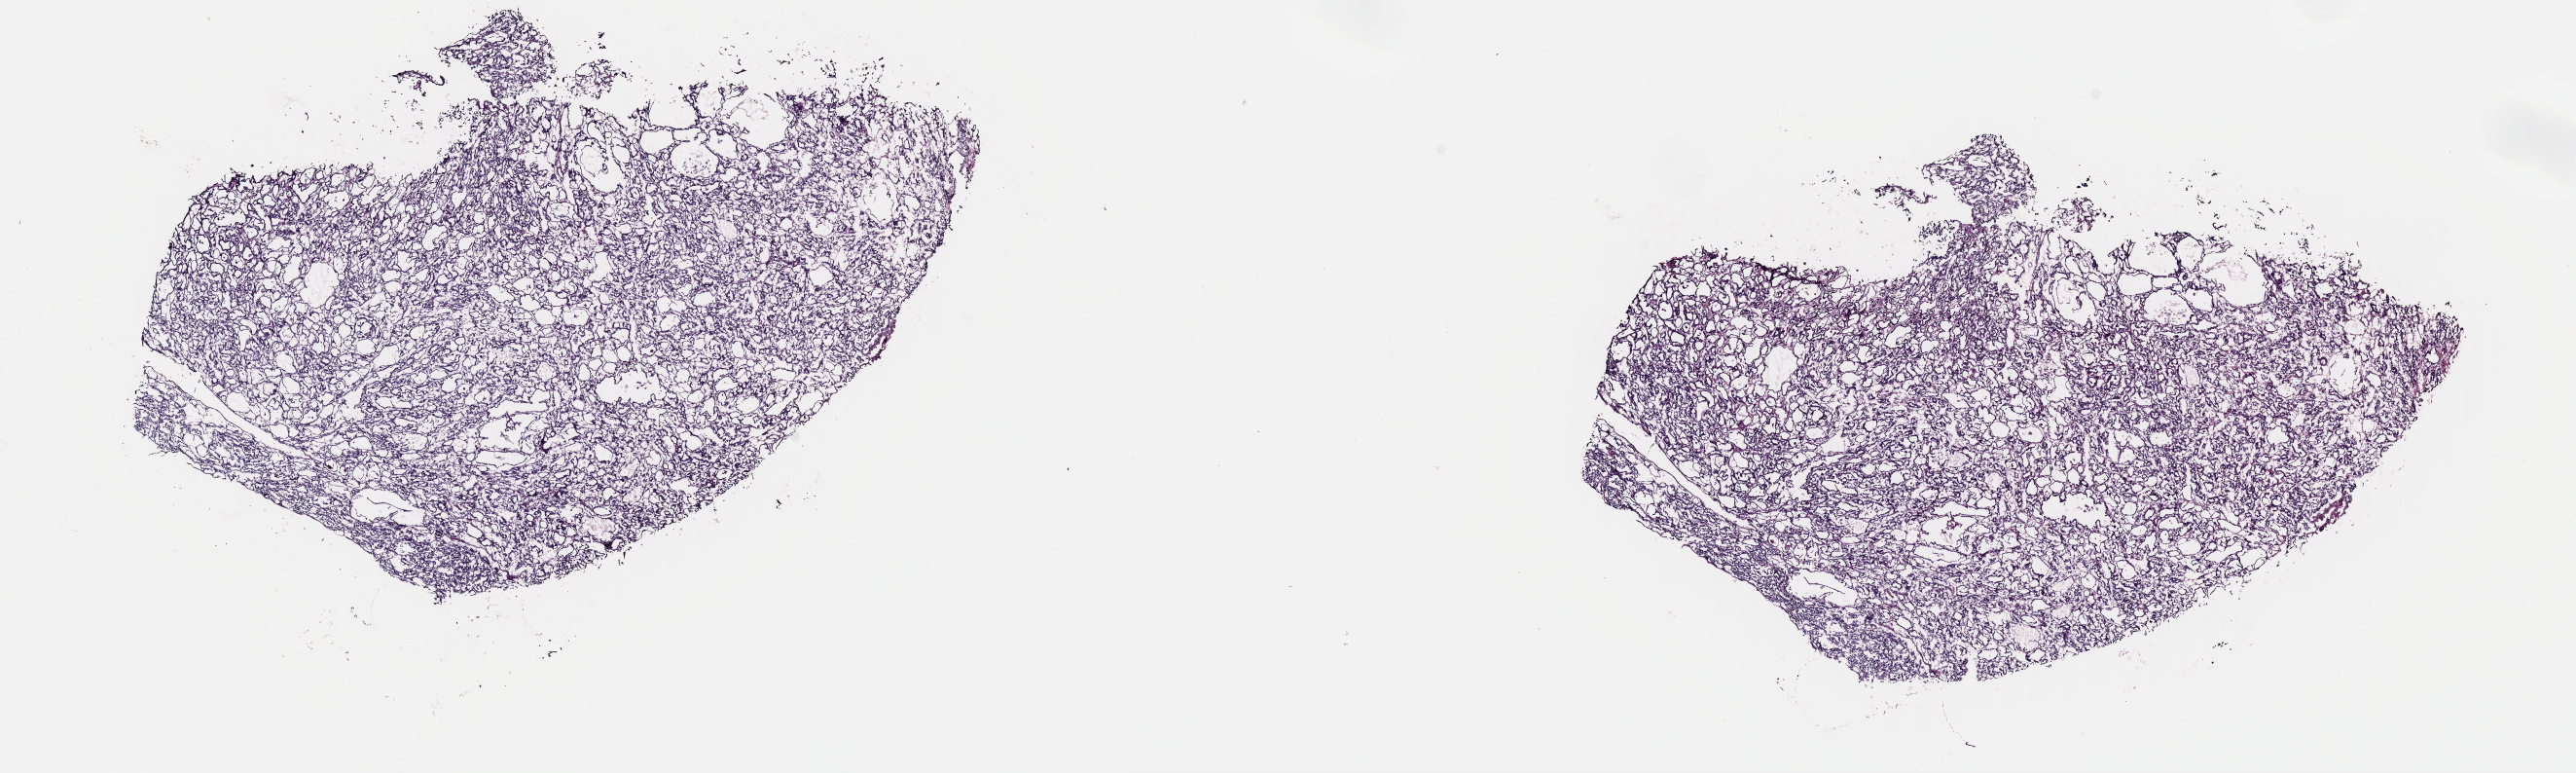
H&E-stained whole-slide image, a low-resolution overview of the entire scanned area, about 20.9 x 6.3 mm (from a 40x scan). Frozen section from the top of the tissue portion. Thyroid, primary tumour sample. Female patient; age at initial diagnosis 46 years. Pathologist review of this section (percent, as recorded): tumour cells 98%, tumour nuclei 99%, normal cells 0%, stromal cells 2%, necrosis 0%. Infiltration values recorded for this section: lymphocyte infiltration 0%, monocyte infiltration 2%, neutrophil infiltration 0%.
Laterality: right. Diagnosis: Papillary carcinoma, follicular variant (thyroid gland). AJCC pathologic stage: II. TNM: T2 N0 MX.